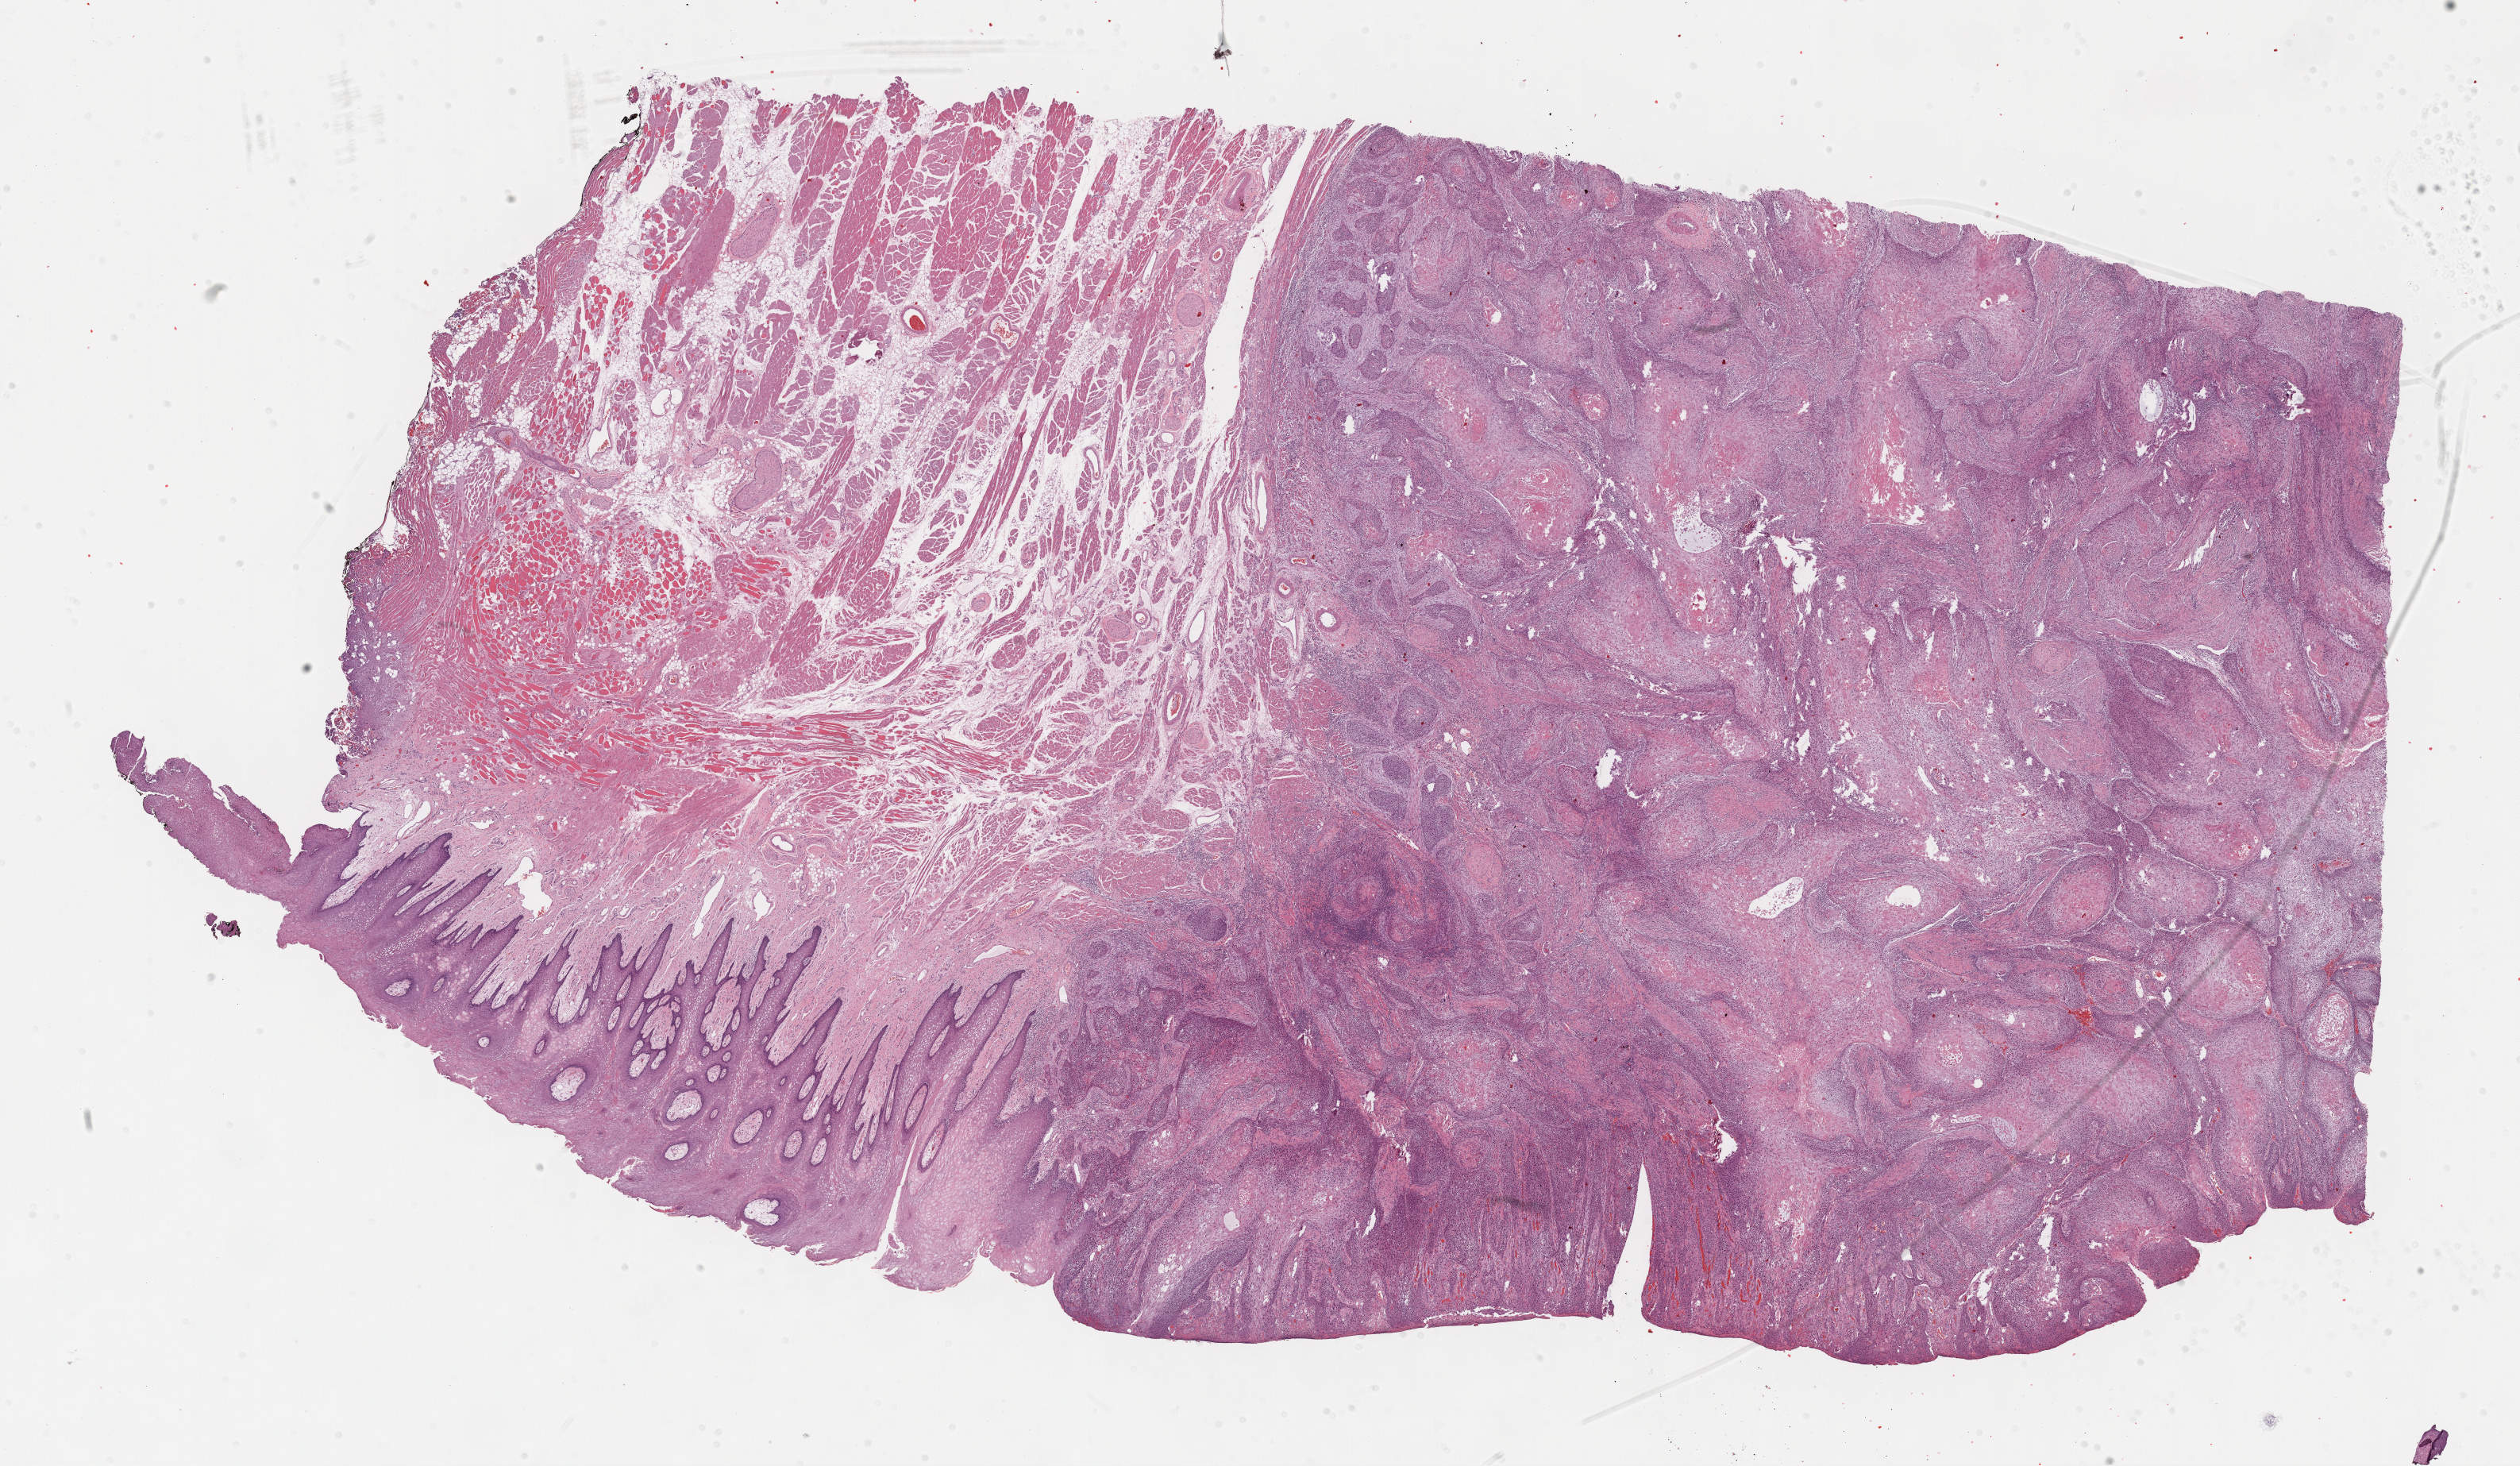
Whole-slide histology image, Hematoxylin and eosin (H&E) stained — shown as a low-resolution overview of the whole scanned area (about 25.7 x 14.9 mm). FFPE section. Sample: primary tumour, head and neck. Male, age 55 years at initial diagnosis. Histologic grade: G1 (well differentiated).
- histologic diagnosis: Squamous cell carcinoma, NOS
- laterality: left
- AJCC pathologic stage: III (7th edition)